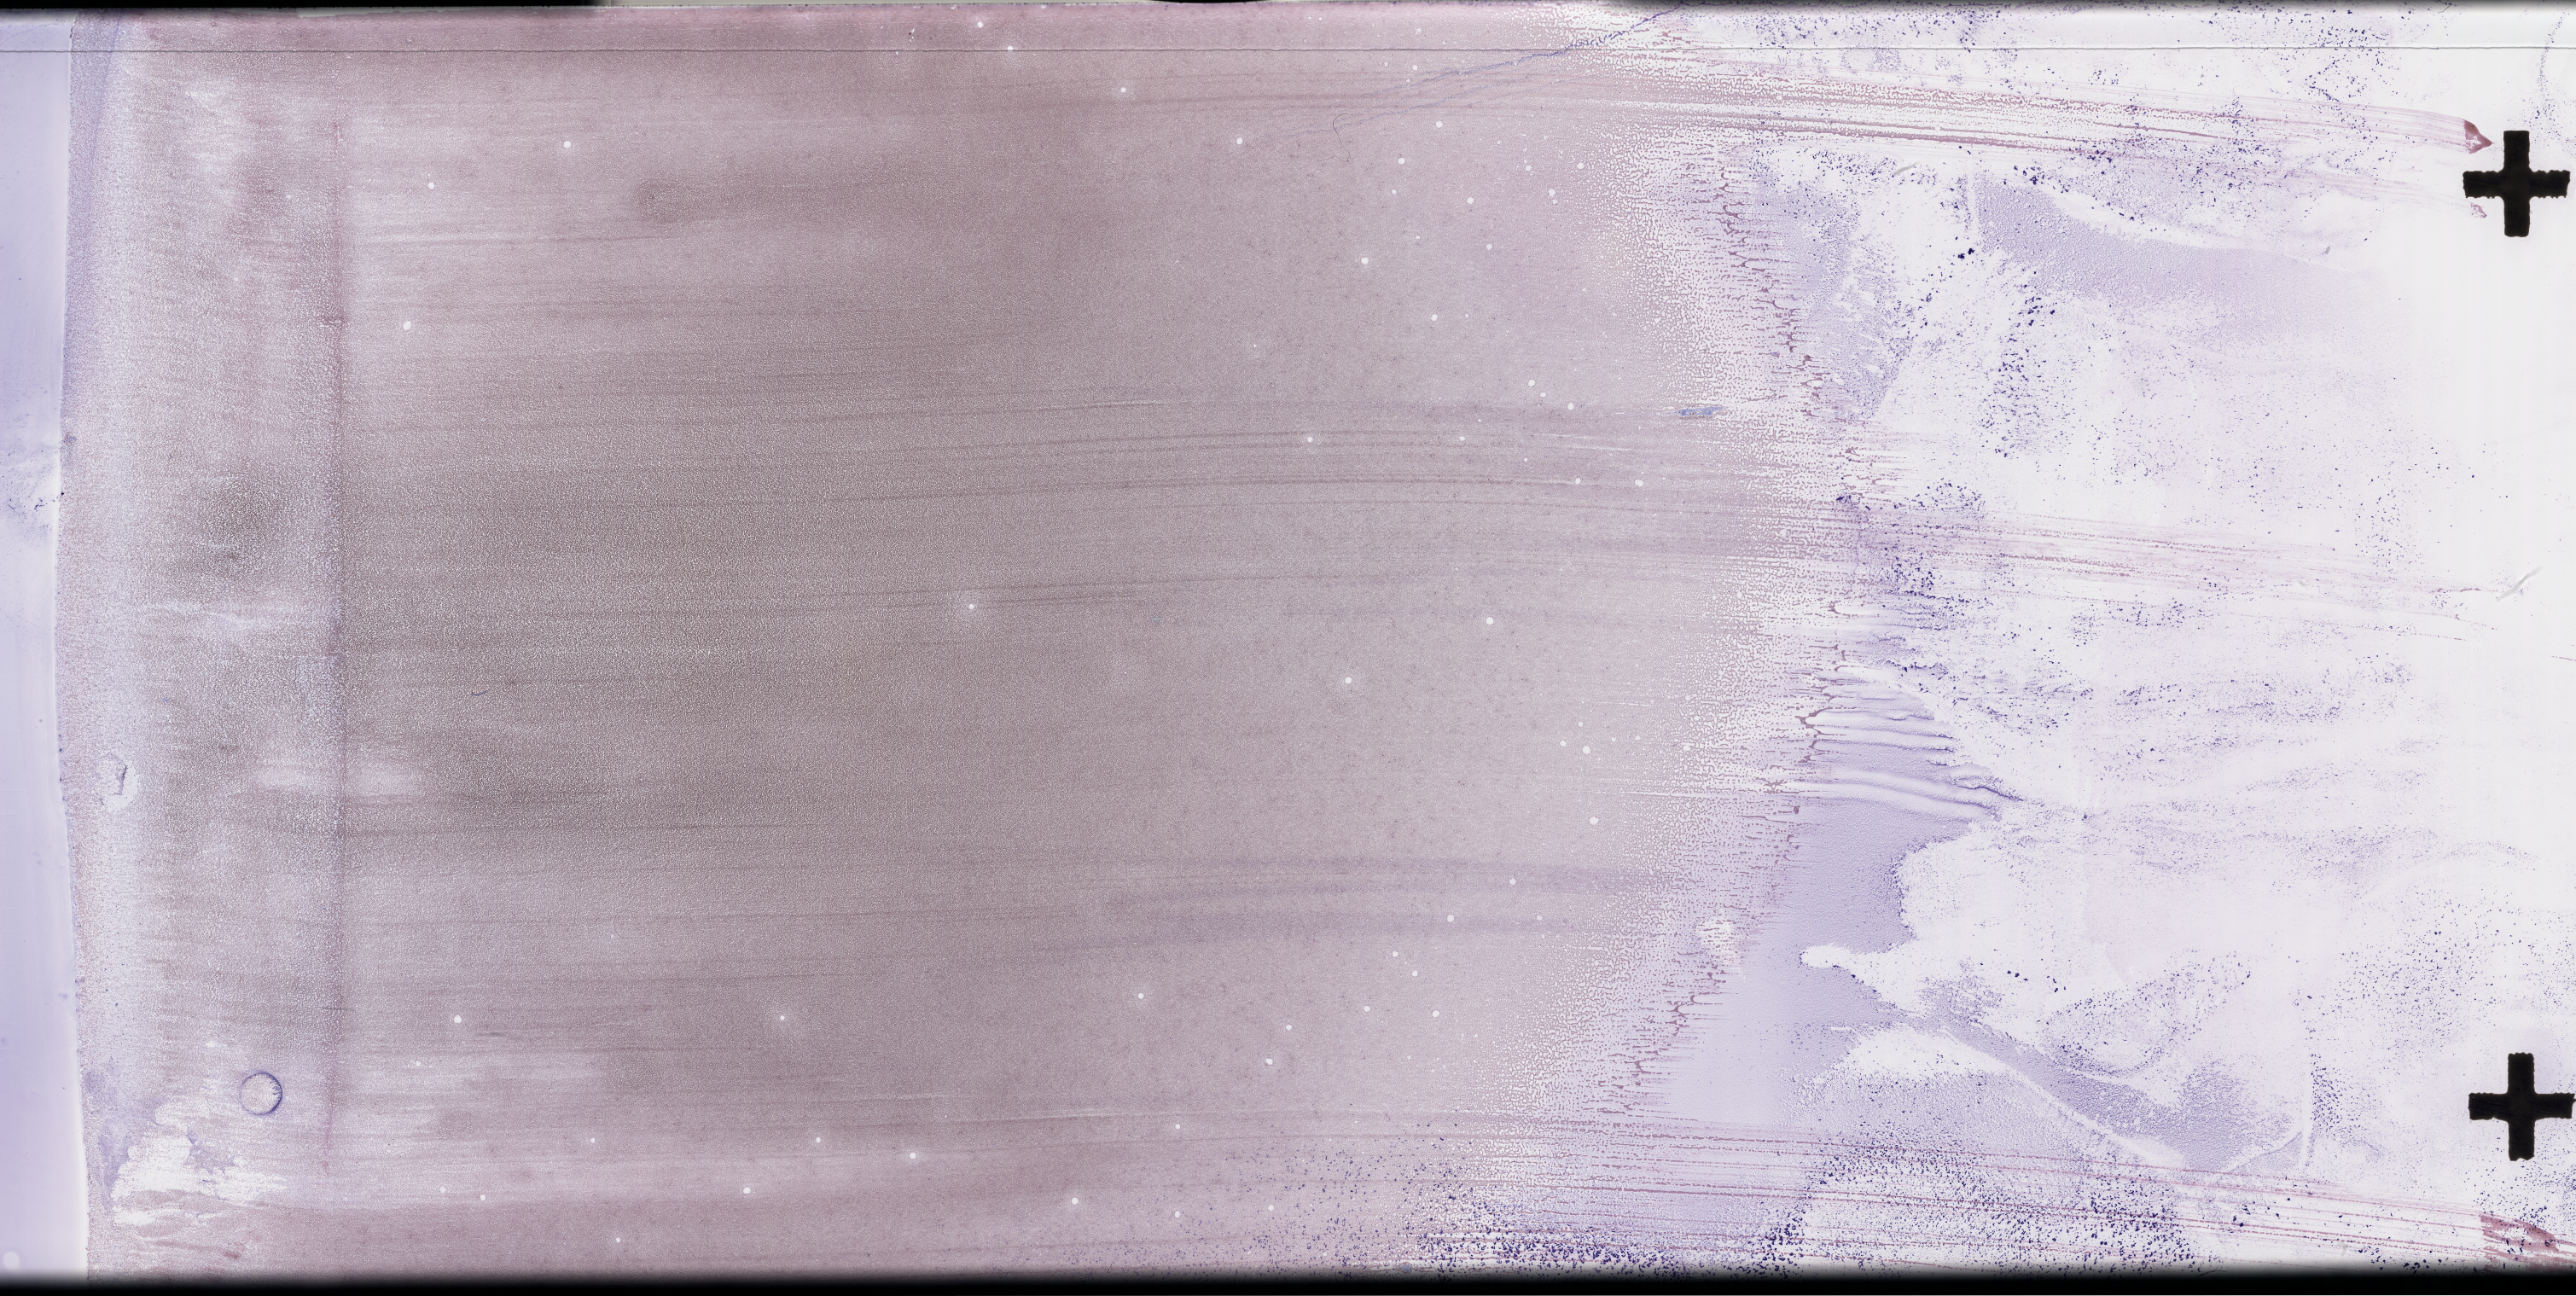
Wright-Giemsa-stained whole blood smear, whole-slide image — shown as a low-resolution overview of the whole scanned area (about 48.8 x 24.5 mm), smear from an EDTA sample, specimen time point: collected on treatment. Patient: female.
From a patient with: Plasma Cell Myeloma.